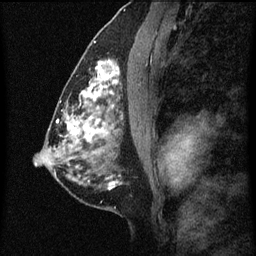
Breast MRI (dynamic contrast-enhanced), one sagittal slice. Position 34 of 60 along the scan axis. Dynamic contrast-enhanced series, image 2 of 7 at this slice position (ordered by acquisition). 1.5 T. TE 4.2 ms, TR 8 ms. 256 × 256 image matrix, field of view 180 × 180 mm. Female patient, age 51 years.
Structures marked on this image (semi-automatic segmentation, software-assisted and operator-edited):
- analysis volume of interest (the breast-tissue region the enhancement analysis was run in; not a lesion): bounding box <86,48,124,101> (left, top, right, bottom; pixels)
- tumour enhancement mask (voxels above the 70 % enhancement threshold inside the analysis volume of interest): <86,62,121,101>